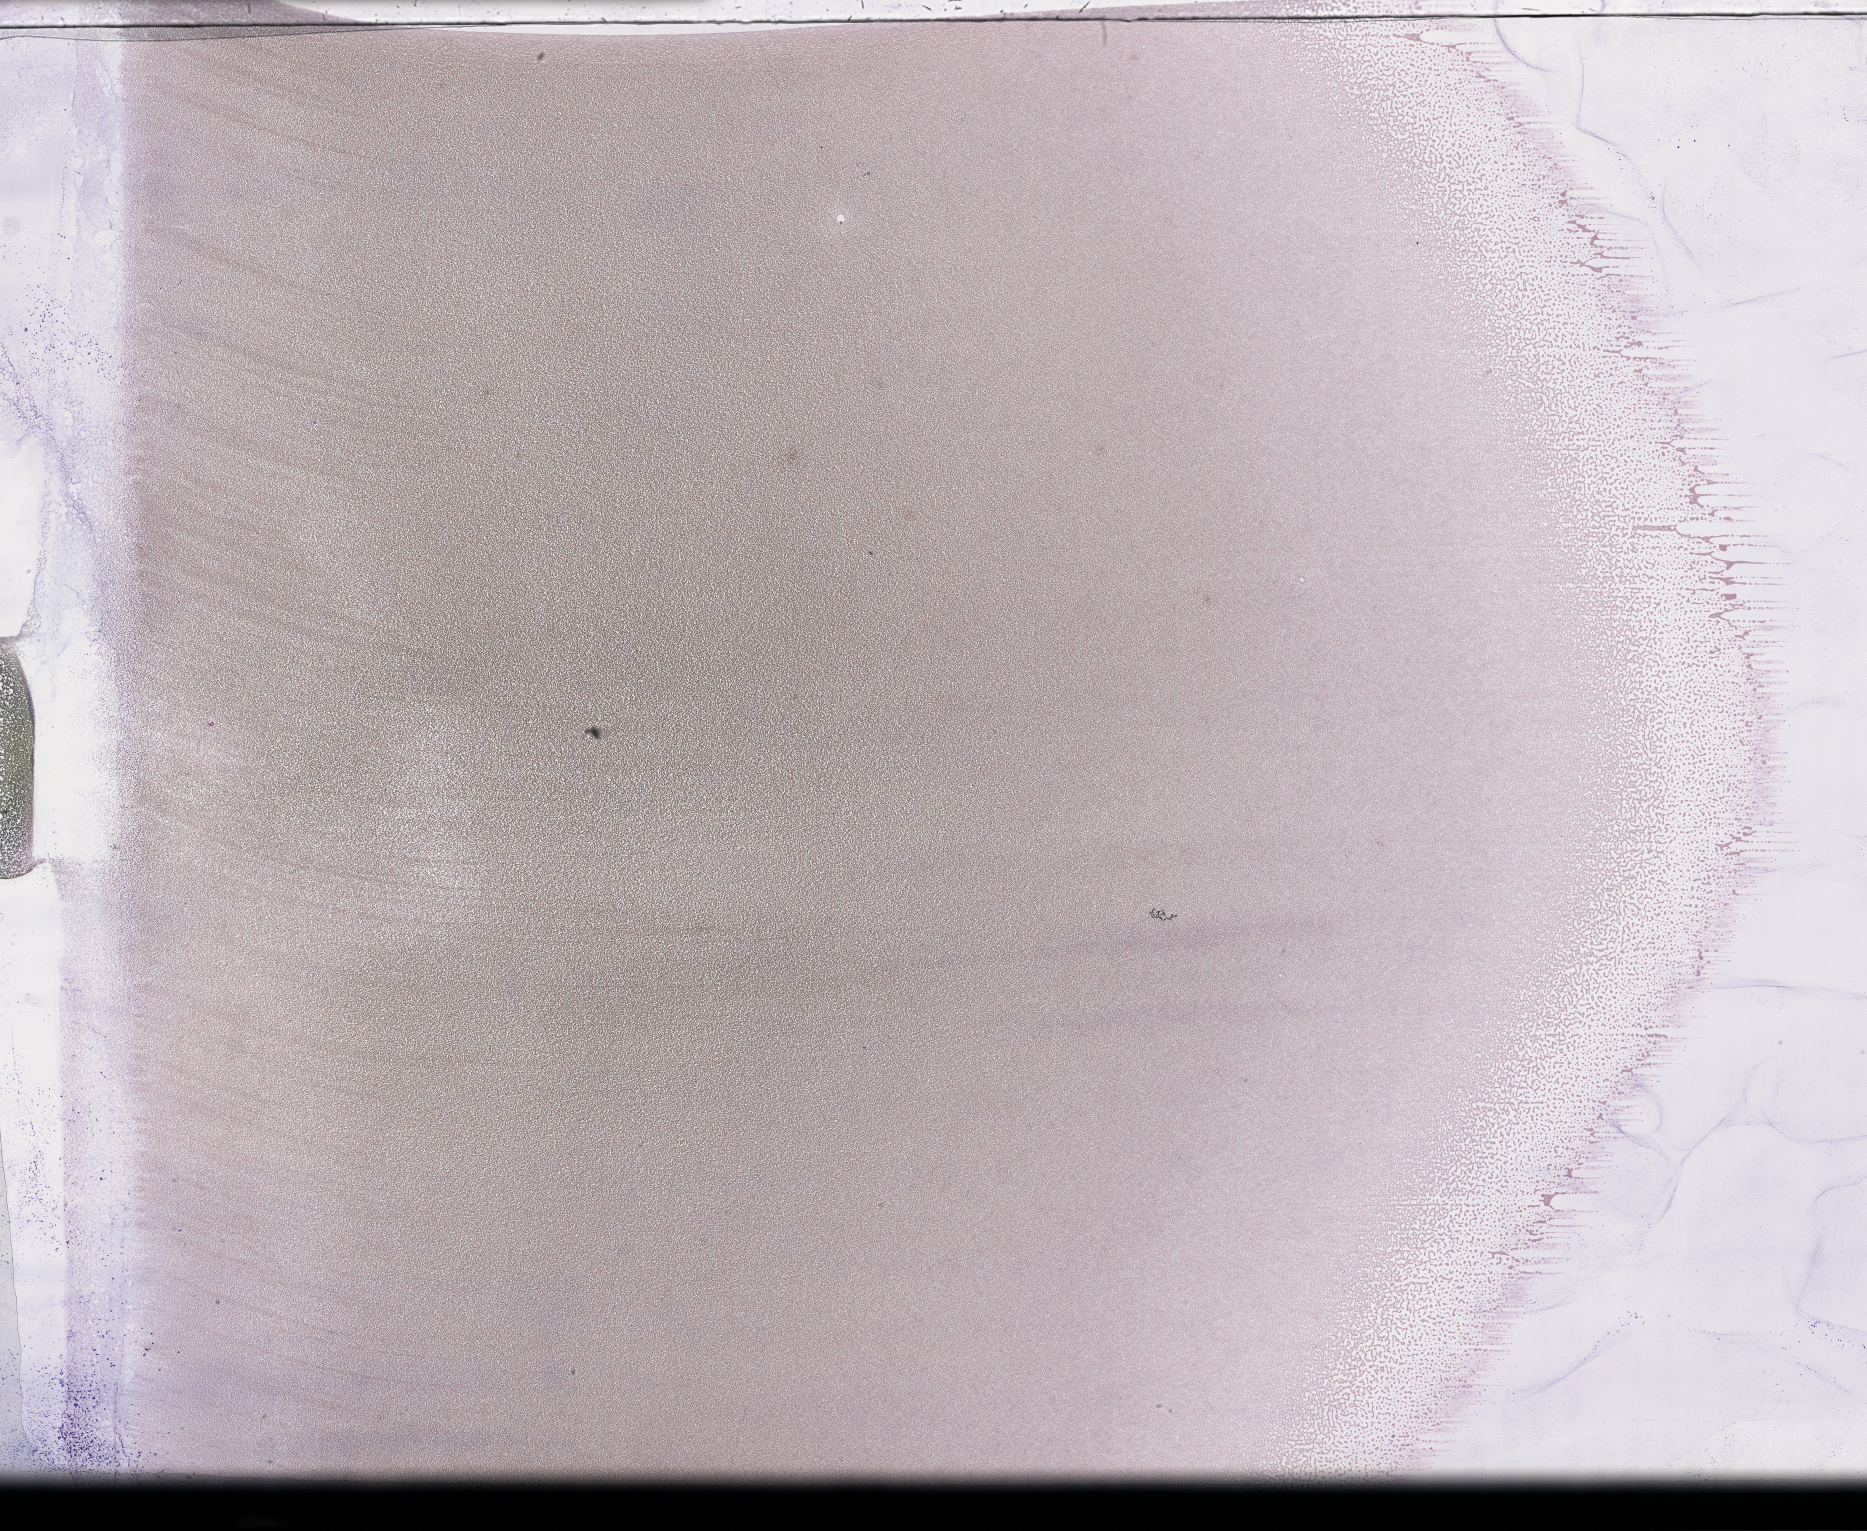
Whole-slide image of a whole blood smear, Wright-Giemsa stain, low-resolution overview of the scanned area, about 30.2 x 24.7 mm, collected on treatment. Patient: female.
From a patient with: Plasma Cell Myeloma.